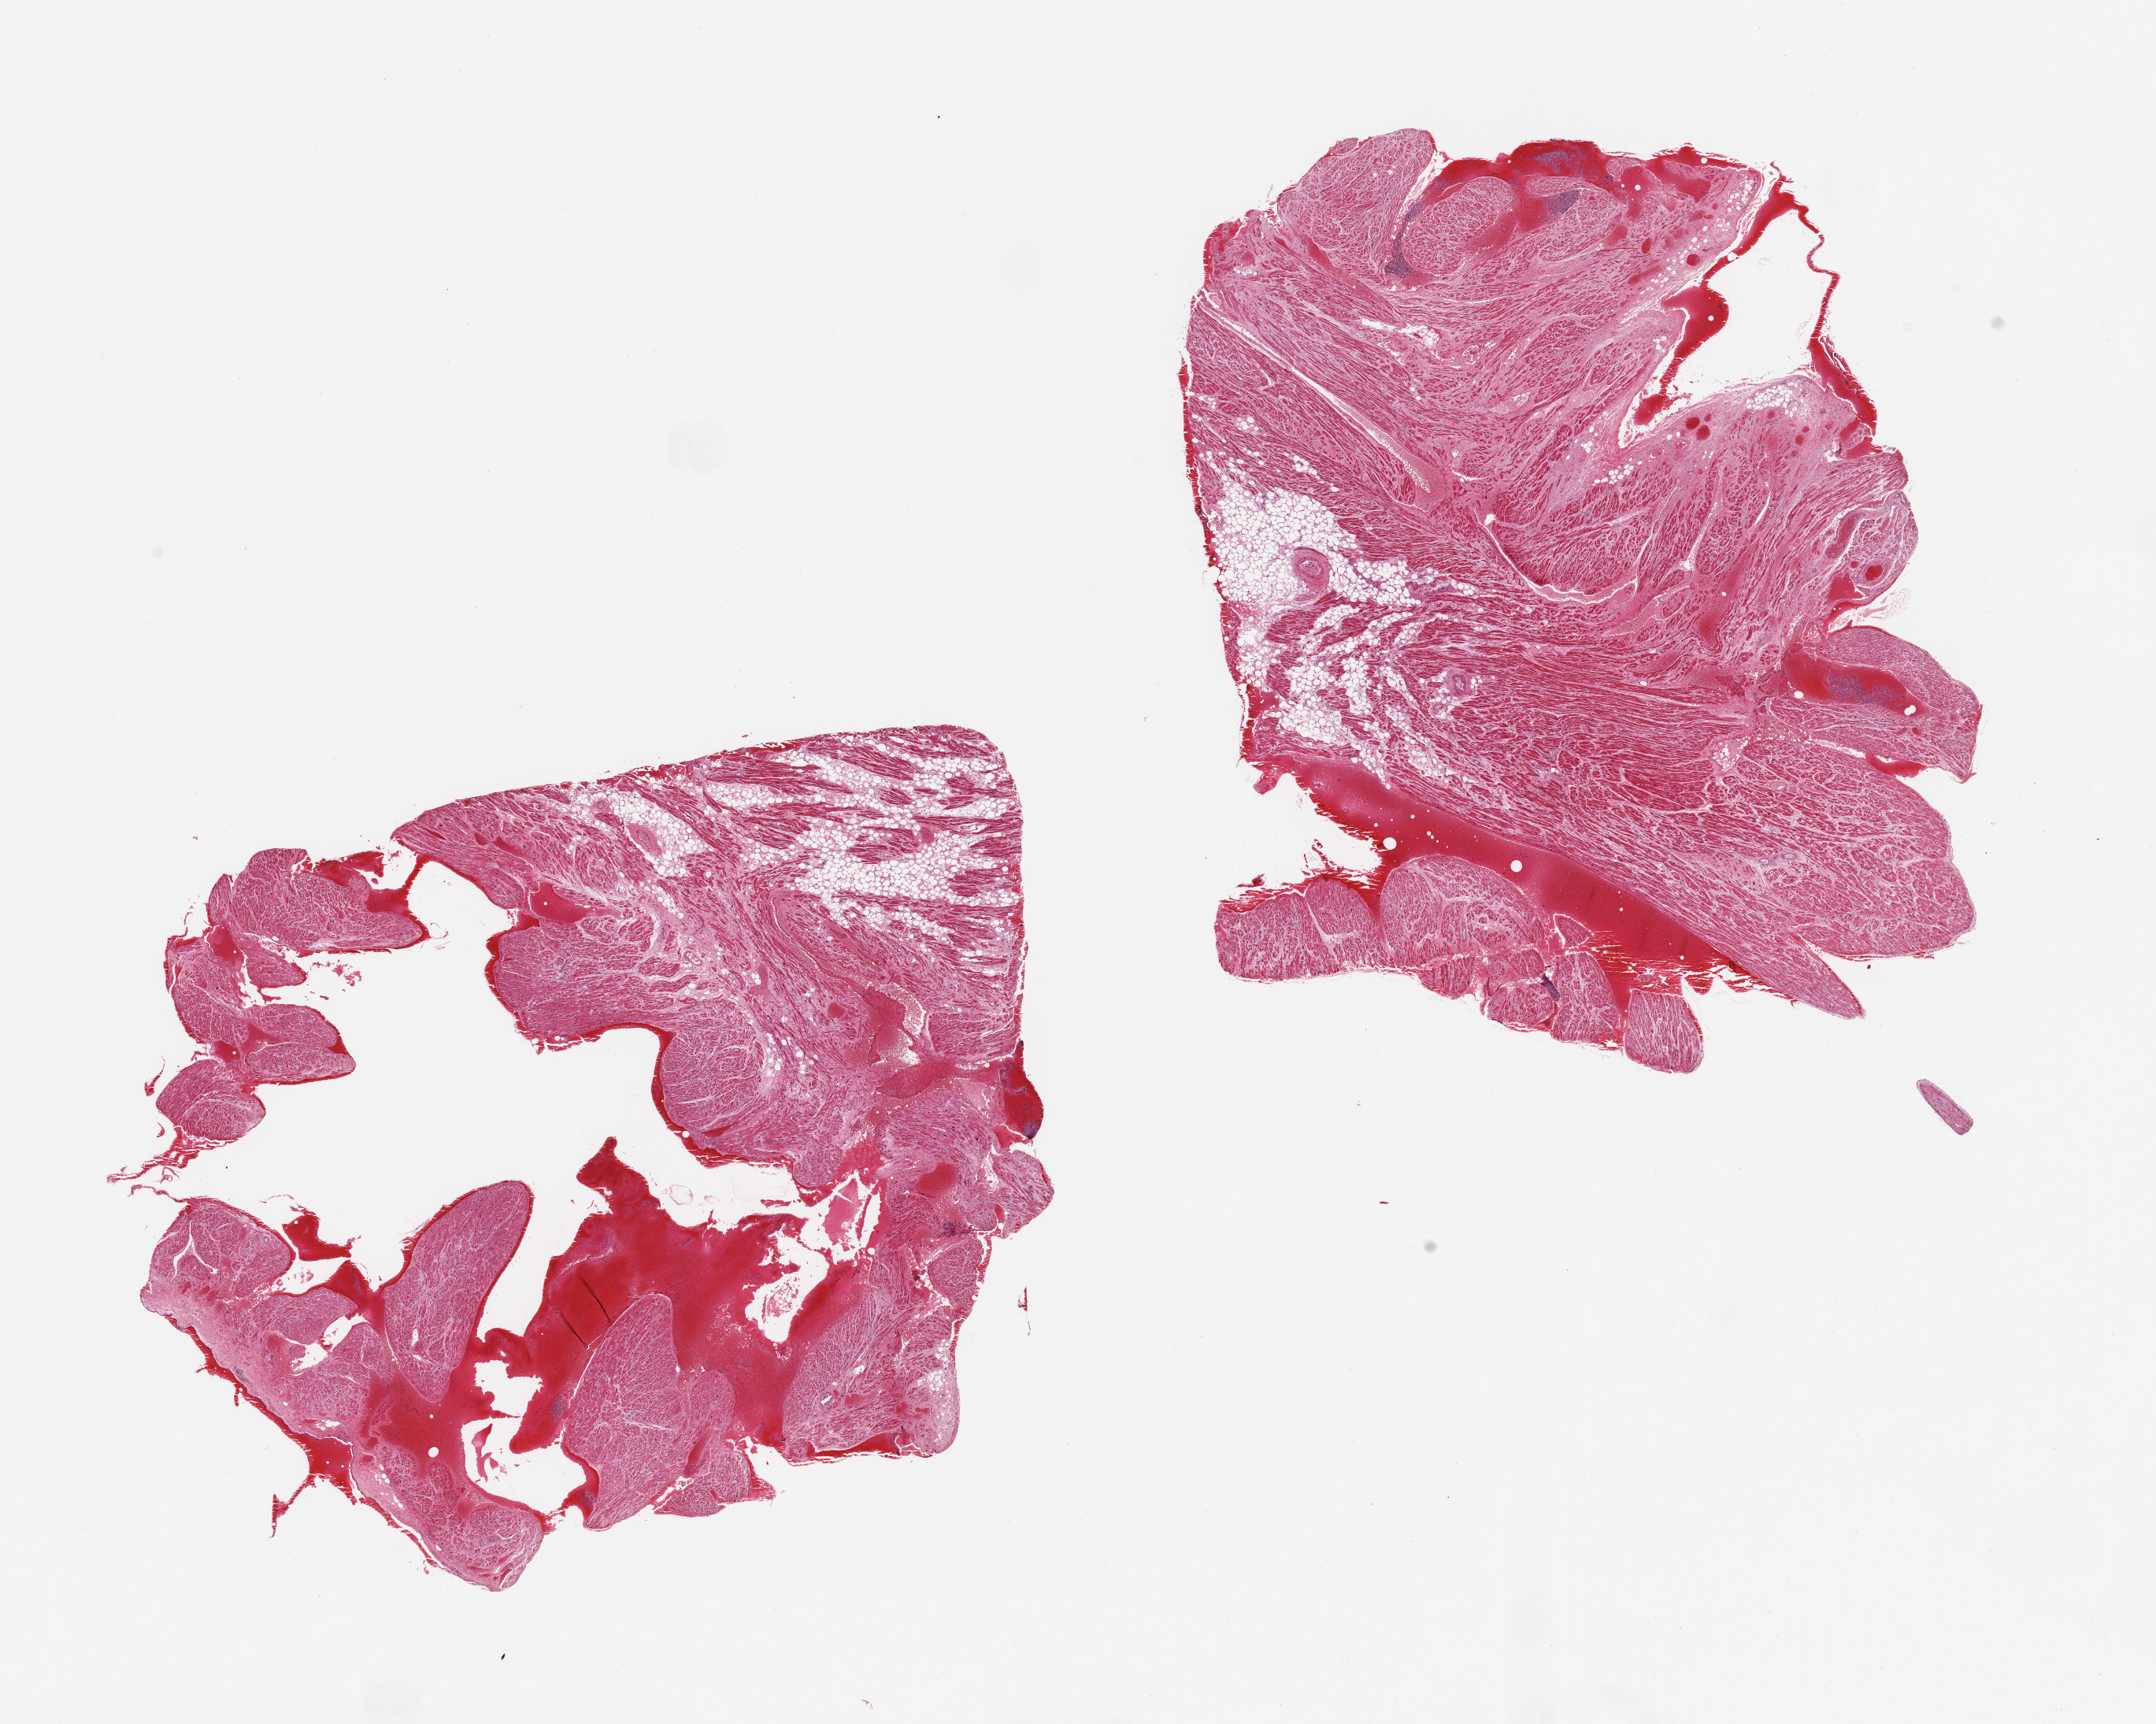
Digitized haematoxylin and eosin-stained section, brightfield — low-resolution overview of the scanned area, about 21.7 x 17.3 mm. PAXgene-fixed paraffin-embedded (PFPE) section. Sampled site (target tissue): auricular appendage. Donor tissue sample. Donor sex: male.
Reviewer comment on this tissue sample: 2 pieces. 10% internal fat. 10% blood in lumen.